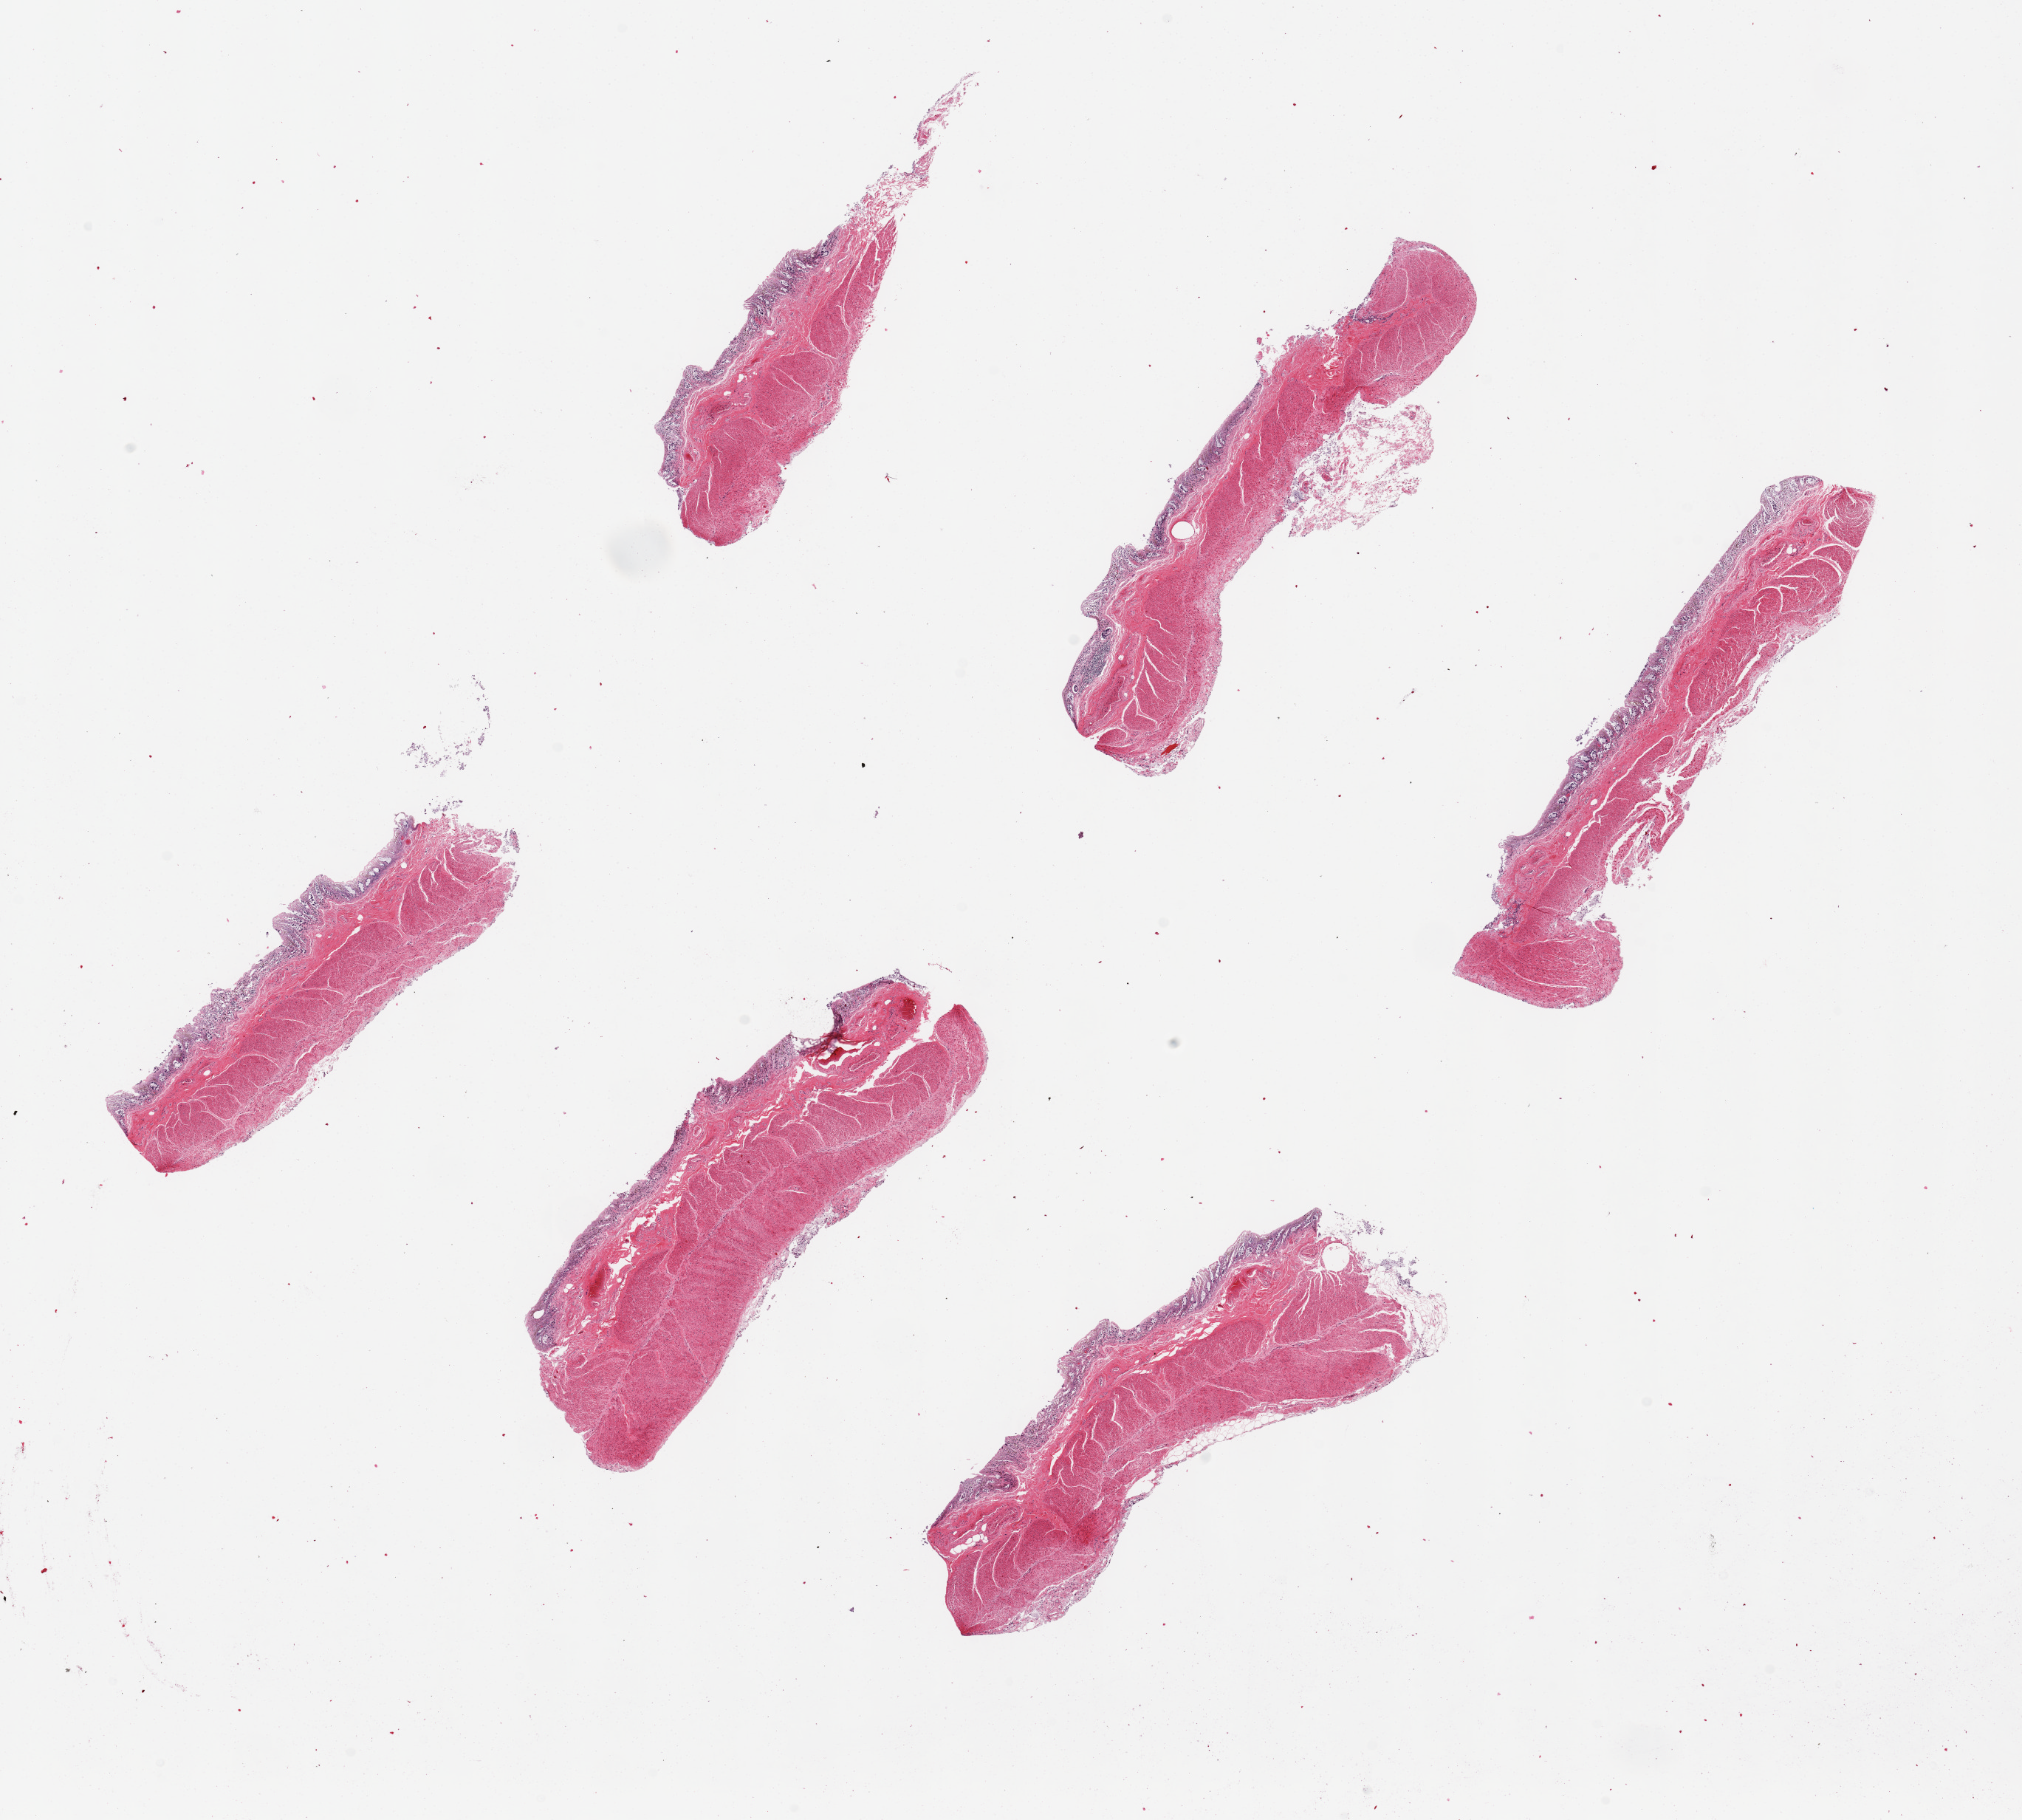
Digitized hematoxylin and eosin (H&E)-stained section, brightfield — low-resolution overview of the scanned area, about 21.7 x 19.5 mm (slide scanned at 20x). PAXgene-fixed, paraffin-embedded tissue. Sampled site (target tissue): transverse colon. Tissue donor sample. Female donor.
* reviewer comment on this tissue sample: 6 pieces, up to 6x2mm; mucosa totally autolyzed; muscle in better shape